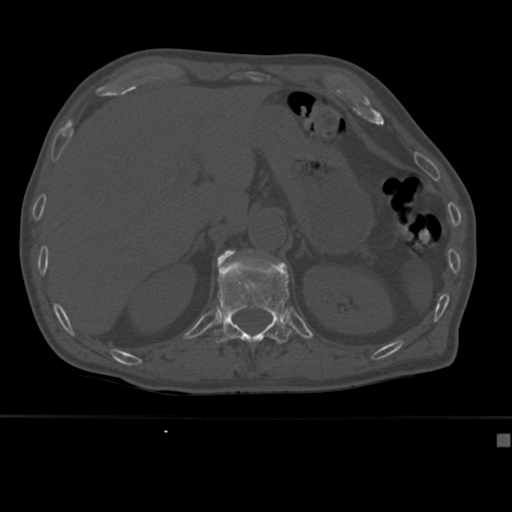
CT including the spine, one axial slice. Slice 190 of 430 in the series (ordered by position). Reconstruction kernel Br40s. 120 kVp. Bone window (W 1800 / L 400 HU). 512 × 512 image matrix, field of view 337 × 337 mm. Patient: male, 64 years. From the clinical record (not read from this slice): primary cancer: uterus.
Outlined on this slice (semi-automatic segmentation, software-assisted and operator-edited):
- L1 vertebra: bounding box <217,250,251,266> (left, top, right, bottom; pixels)
- T12 vertebra: <214,251,292,346>